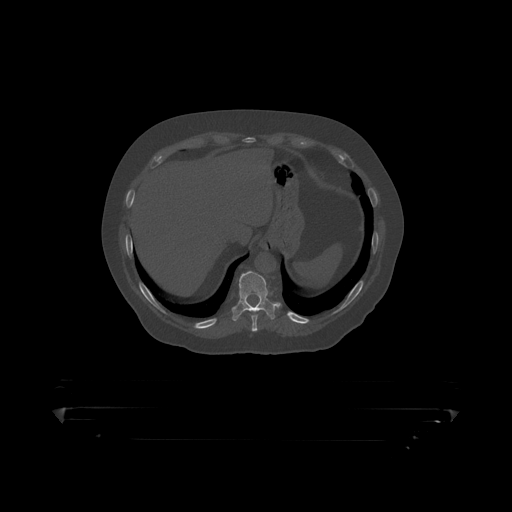
CT including the spine, one axial slice; slice 220 of 390 in the series (ordered by position); reconstruction kernel STANDARD; bone window (W 1800 / L 400 HU); 512 × 512 image matrix, field of view 650 × 650 mm. Patient: male, 60 years. Case-level facts recorded for this patient, not image findings: primary cancer: prostate.
Outlined on this slice (semi-automatically segmented with operator editing):
- T10 vertebra: bounding box [x1, y1, x2, y2] px = [232, 271, 278, 318]
- T9 vertebra: [251, 313, 258, 319]